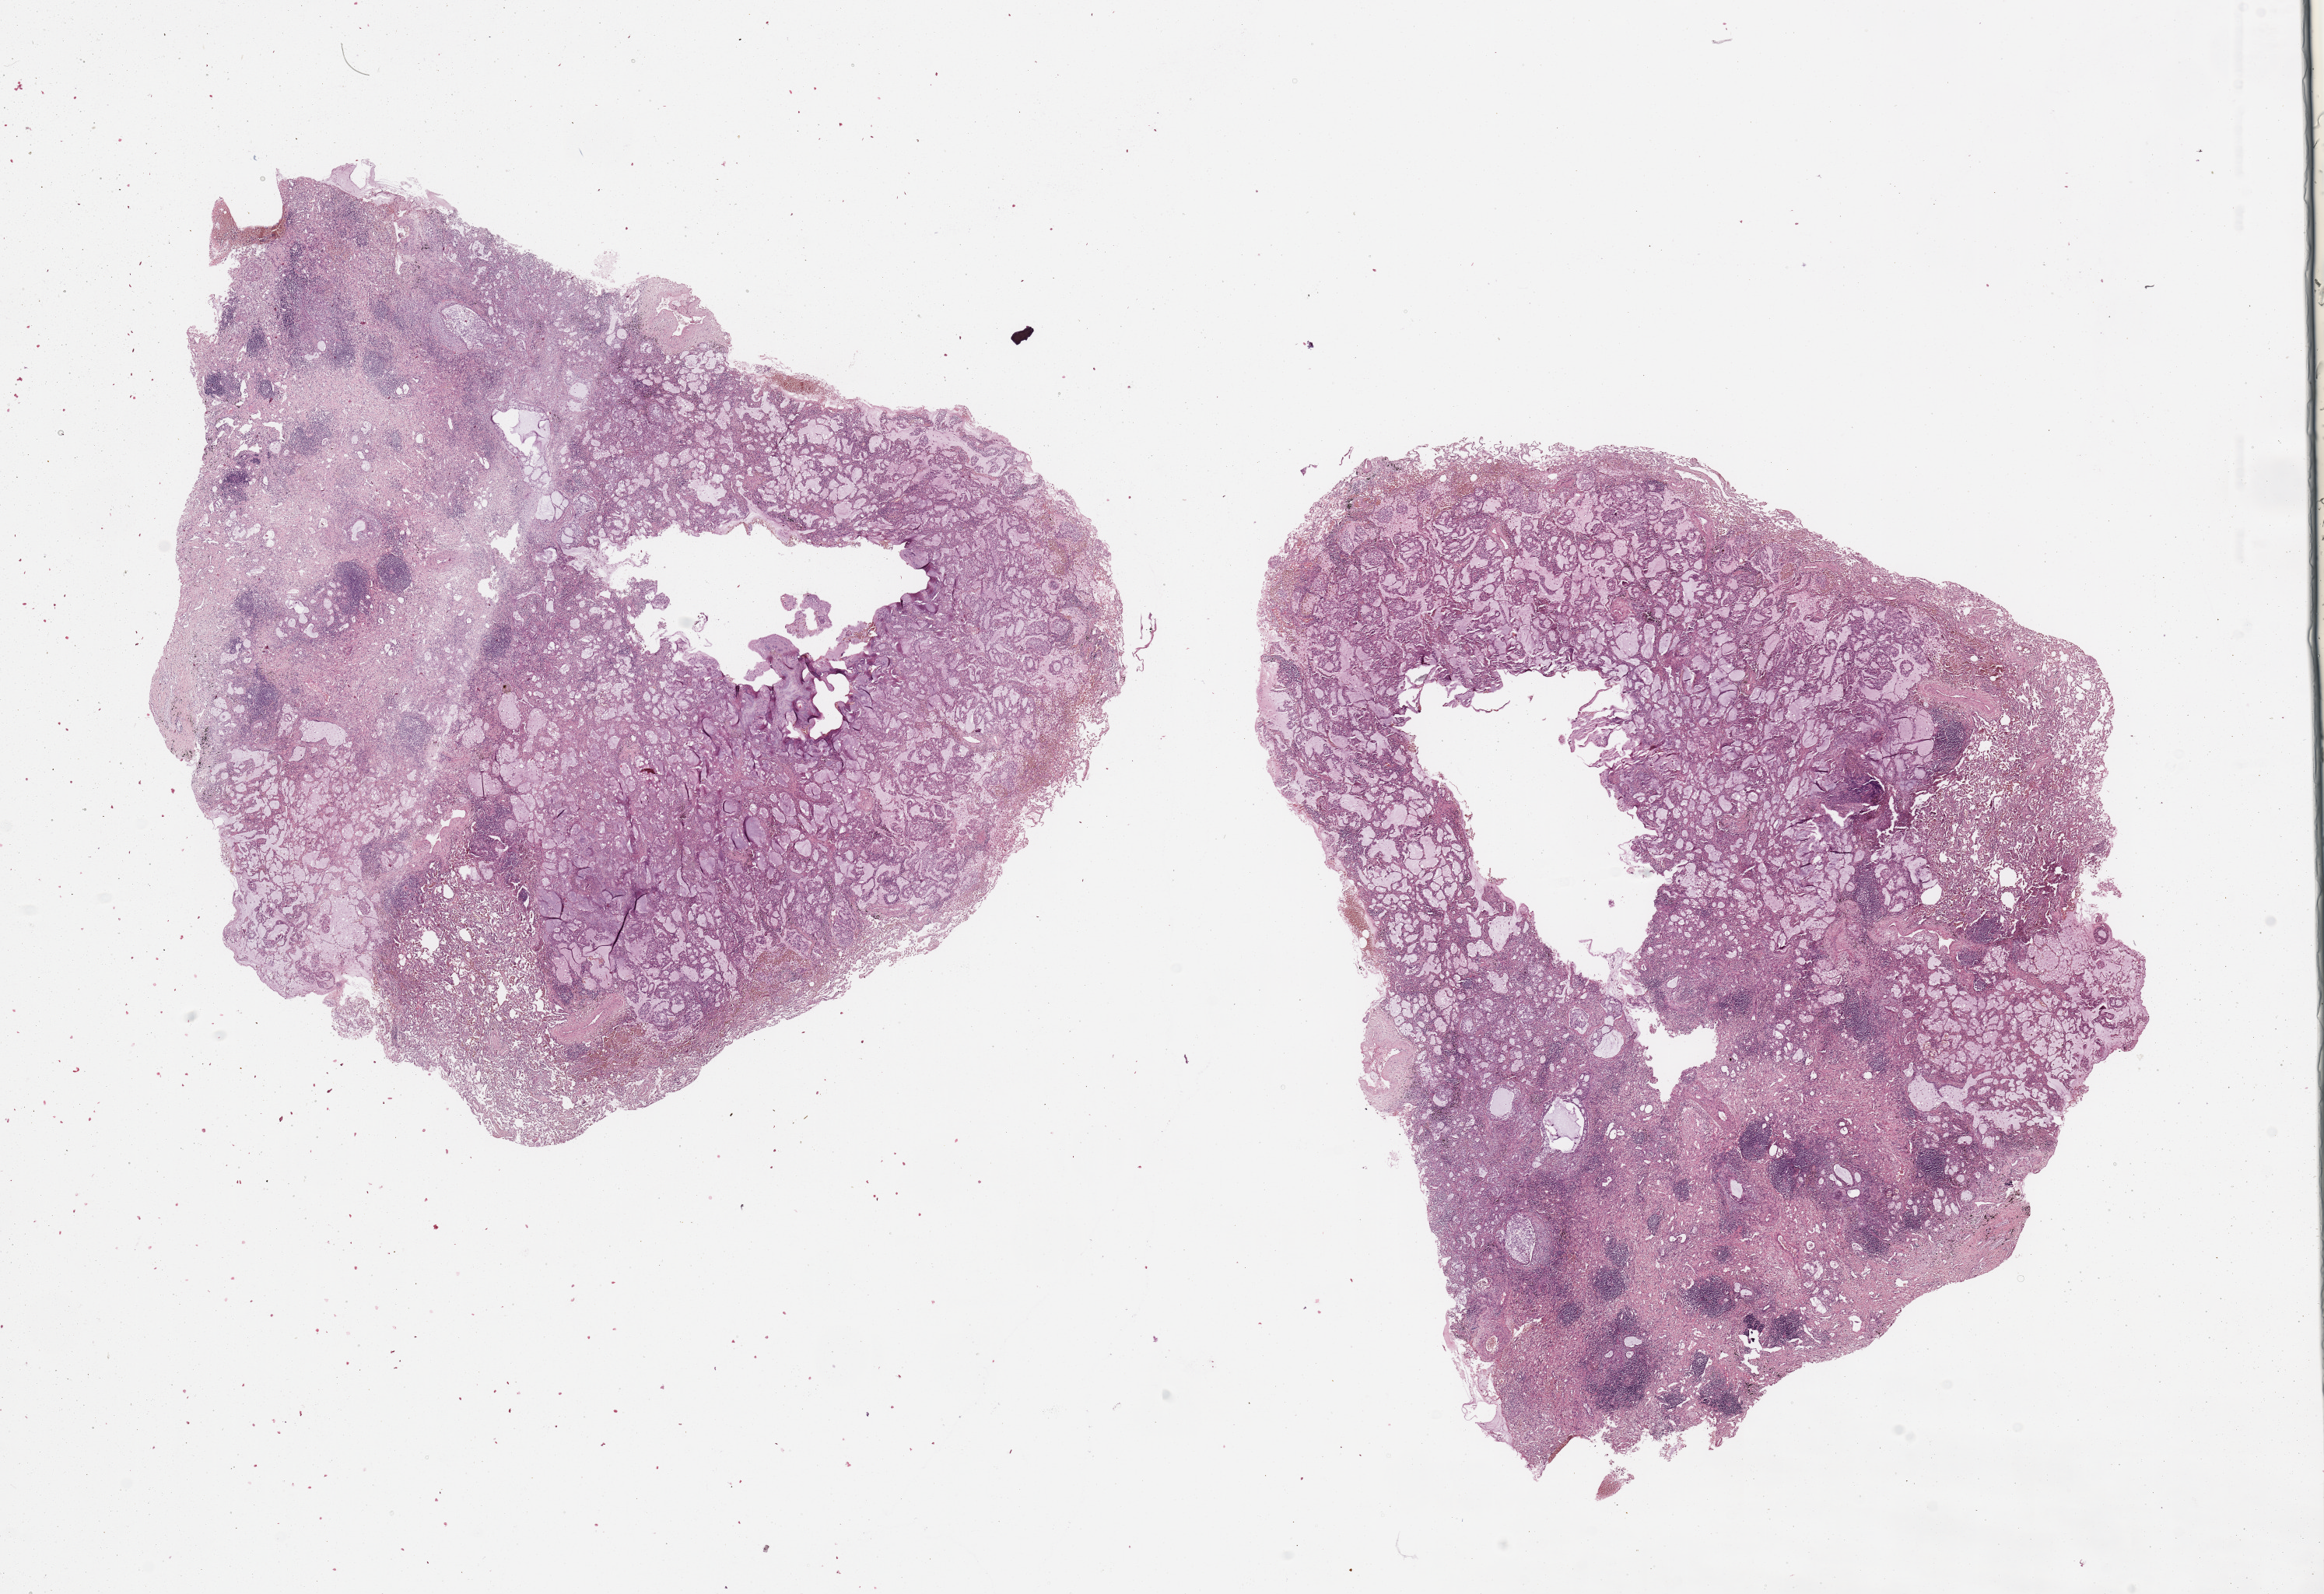
Whole-slide histology image, H&E-stained — whole scanned area (about 23.6 x 16.2 mm, slide scanned at 20x) shown as a low-resolution overview; tumour tissue sample, lung. Patient: male, age 47 years.
Histologic diagnosis: Adenocarcinoma, NOS.